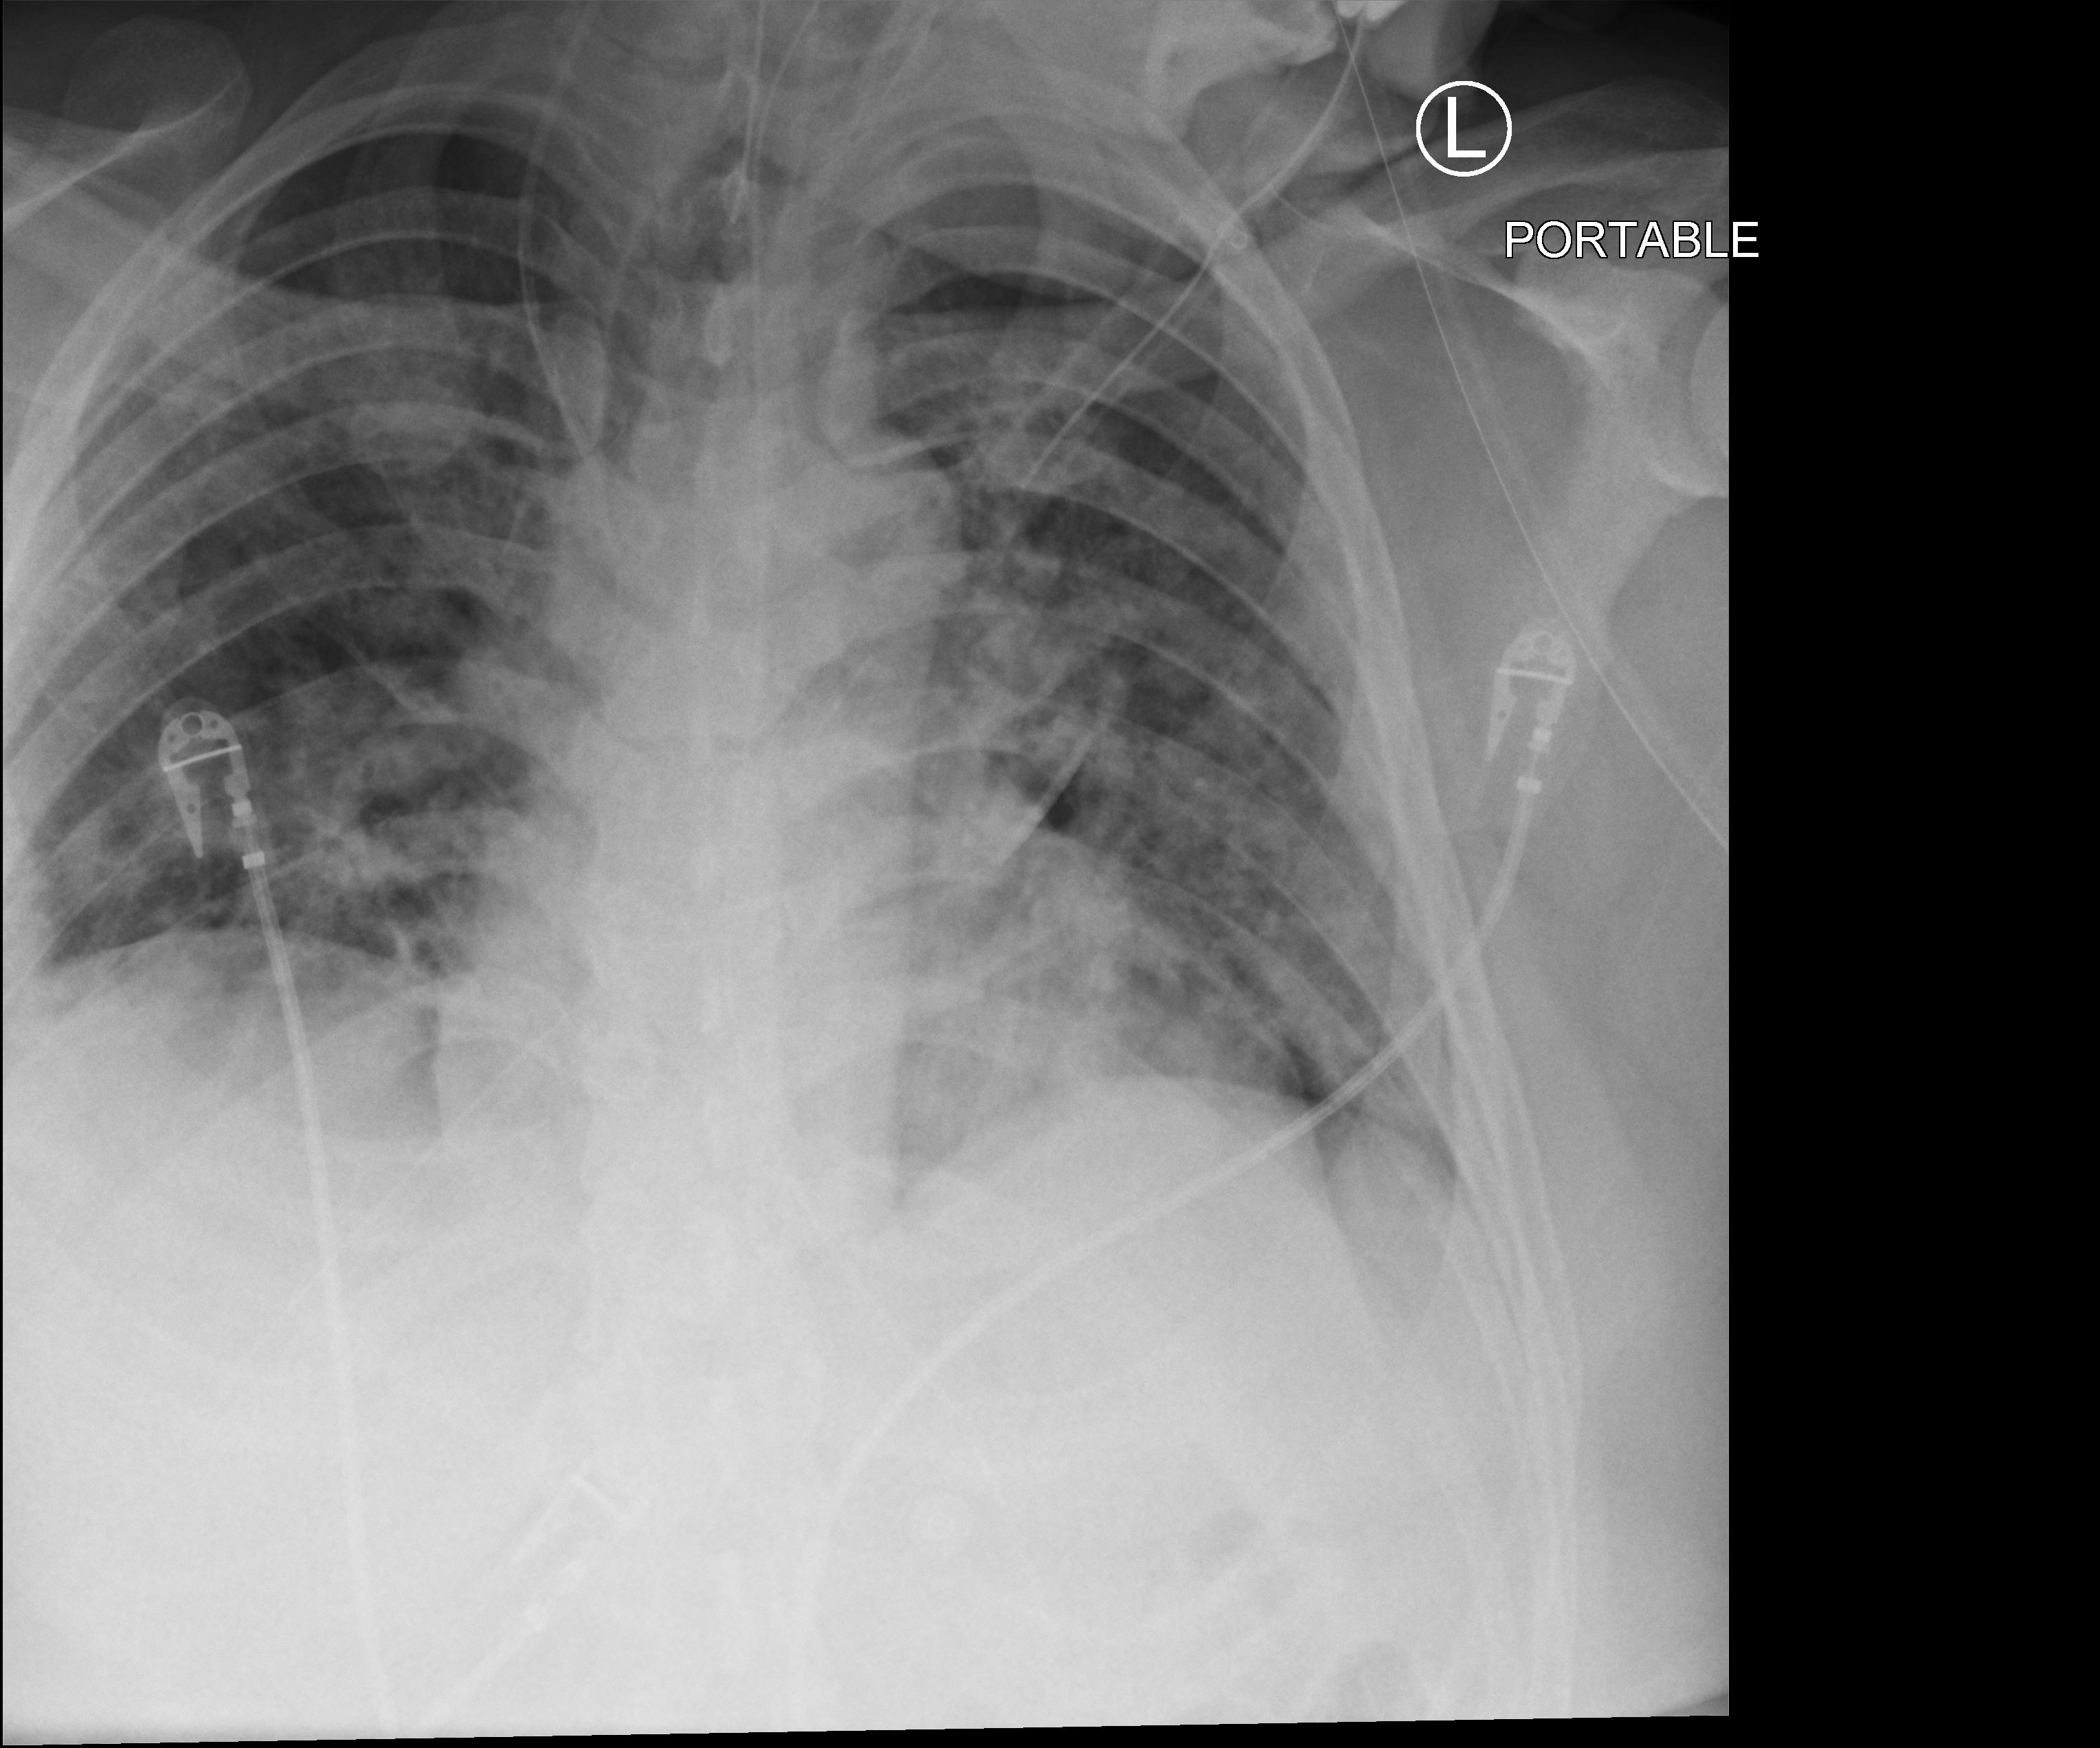
Bedside chest radiograph (computed radiography), anteroposterior (AP) projection. Male patient hospitalised with COVID-19, age 18–59 years.
Admission-level facts for this patient (not findings on this image; timing relative to this image not recorded): mechanically ventilated during this hospital stay: yes; admitted to intensive care during this hospital stay: yes.